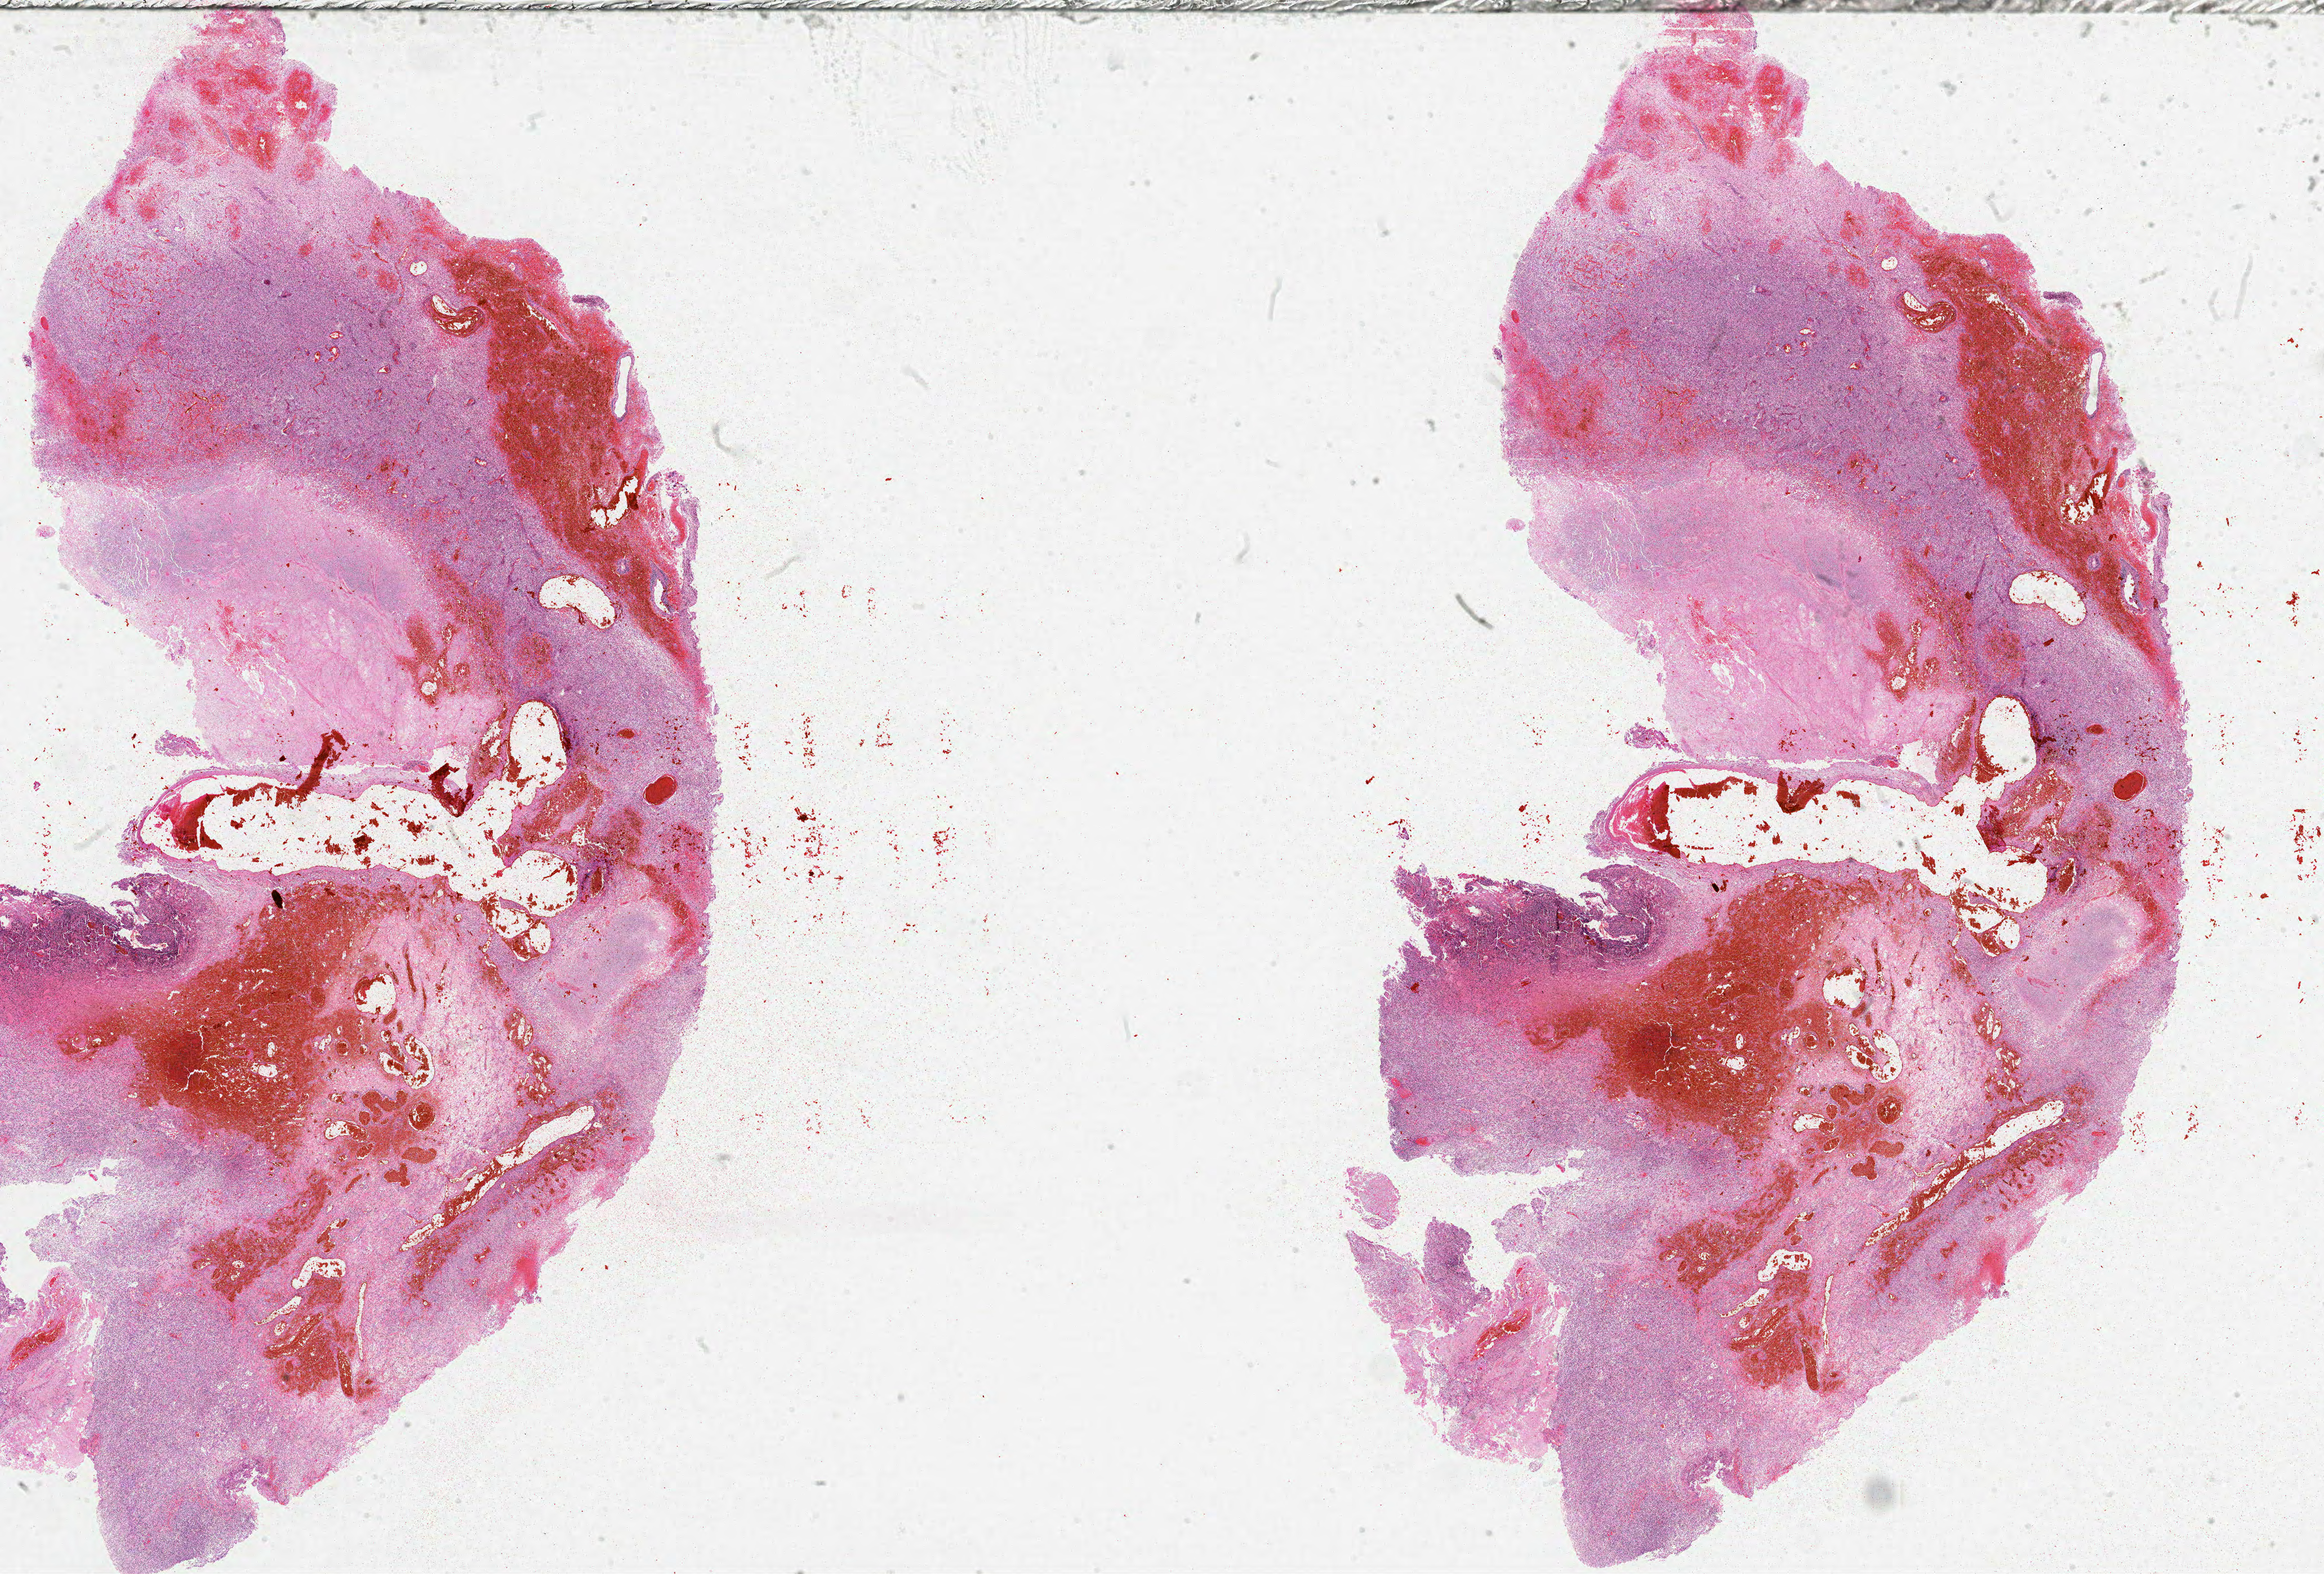
Hematoxylin and eosin (H&E) stained whole-slide image, shown as a low-resolution overview of the whole scanned area (about 33.0 x 22.3 mm, slide scanned at 20x), FFPE section, brain, primary tumour sample. Patient: male, age at initial diagnosis 69 years.
Pathologic diagnosis: Glioblastoma.